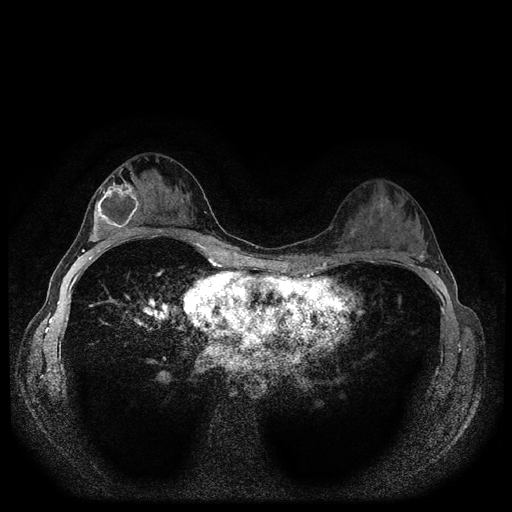
Breast MRI (dynamic contrast-enhanced, multi-phase), one axial slice. Slice 61 of 116 in the series (ordered by position). Dynamic contrast-enhanced series, time point 2 of 5 at this slice position (early post-contrast). 1.5 T. TE 2.7 ms, TR 5.4 ms. 512 × 512 image matrix. Patient: female, 29 years.
Structures marked on this image (semi-automatically segmented with operator editing):
- breast lesion (labelled 'tumour' in the annotation; benign lesions carry a separate 'benign' label): bounding box (x1, y1, x2, y2) in pixels: (88, 180, 141, 243)